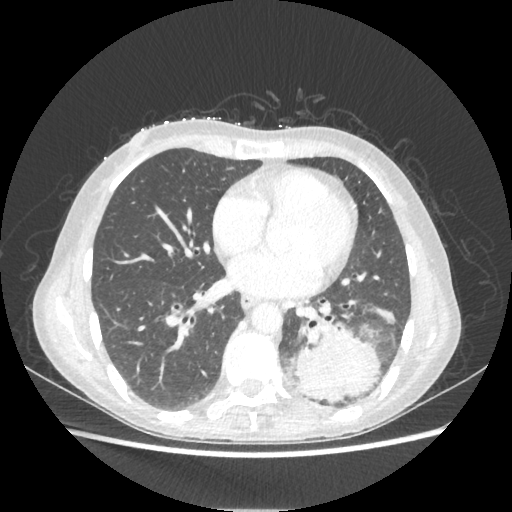
Chest CT, one axial slice; slice 96 of 221 in the series (ordered by position); reconstruction kernel STANDARD; 80 kVp; lung window (W 1500 / L -600 HU); 1.25 mm slice thickness; 512 × 512 image matrix, field of view 360 × 360 mm. Patient: female, 53 years. Case-level facts recorded for this patient, not image findings: clinical TNM (as recorded): T3 N0 M0.
Structures marked on this image (bounding box drawn by a radiologist):
- lung tumour (recorded histology: adenocarcinoma): bounding box <293,318,380,401> (left, top, right, bottom; pixels)